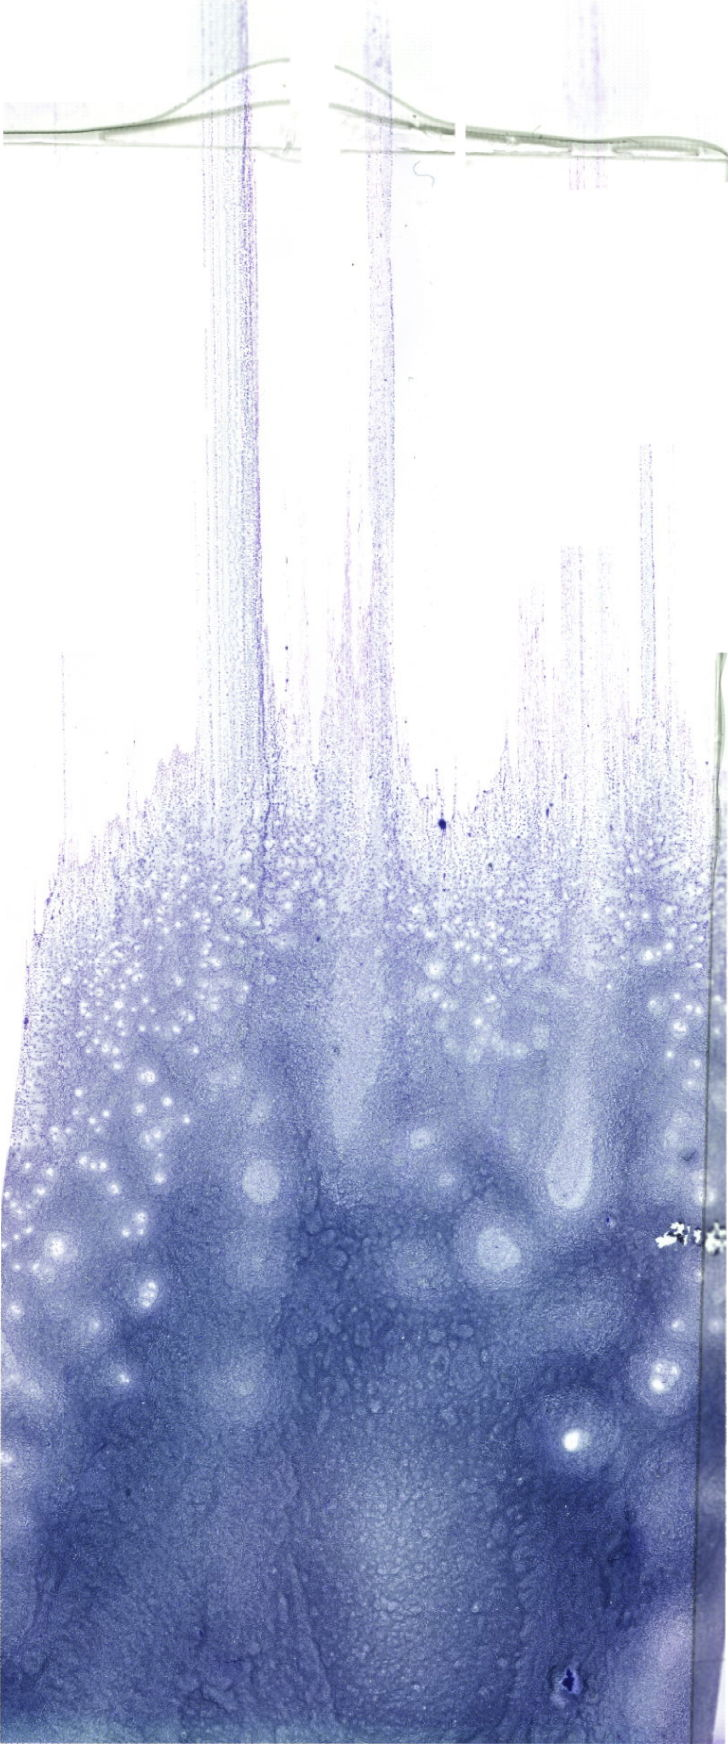
Whole-slide image of a May-Grünwald–Giemsa-stained bone marrow aspirate smear — shown as a low-resolution overview of the whole scanned area (about 20.6 x 49.4 mm). Male patient.
Diagnosis: B Acute Lymphoblastic Leukemia.